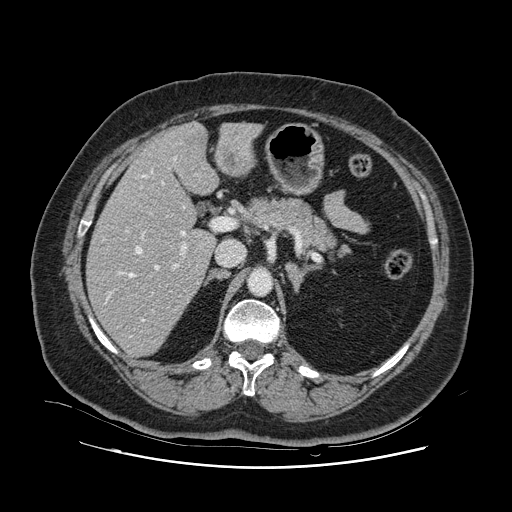
Contrast-enhanced abdominal CT, one axial slice. Position 61 of 132 along the scan axis. 120 kVp. Intravenous contrast given. Soft-tissue window (W 400 / L 40 HU). 2.5 mm slice thickness. 512 × 512 image matrix, field of view 391 × 391 mm. Female patient, age 73 years. Case-level facts recorded for this patient, not image findings: diagnosis: colorectal cancer liver metastases, imaged before liver resection; multiple liver metastases: no; largest metastasis: 7 cm; disease in both lobes: no.
Annotated regions visible in this slice (outlined manually by an expert reader):
- hepatic veins: bounding box <106,157,186,322> (left, top, right, bottom; pixels)
- liver: <88,124,257,356>
- planned liver remnant (the part of the liver to remain after resection): <88,150,215,356>
- portal vein (with intrahepatic branches): <127,217,226,312>
- liver metastasis: <224,152,238,171>